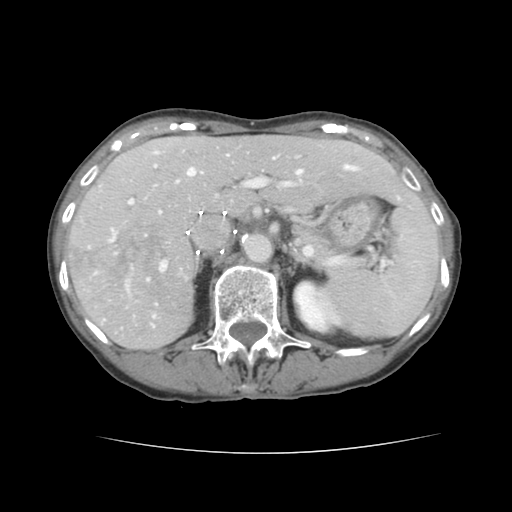
Contrast-enhanced abdominal CT, one axial slice; slice 90 of 136 in the series (ordered by position); 120 kVp; intravenous contrast given; soft-tissue window (W 400 / L 40 HU); 2.5 mm slice thickness; 512 × 512 image matrix. Female patient, age 77 years. From the clinical record (not read from this slice): diagnosis: colorectal cancer liver metastases, imaged before liver resection; multiple liver metastases: yes; largest metastasis: 3 cm; disease in both lobes: no.
Annotated regions visible in this slice (expert manual segmentation):
- hepatic veins: bounding box <151,152,356,327> (left, top, right, bottom; pixels)
- liver: <68,136,424,349>
- planned liver remnant (the part of the liver to remain after resection): <153,136,421,214>
- portal vein (with intrahepatic branches): <110,164,399,281>
- liver metastasis: <89,225,166,278>